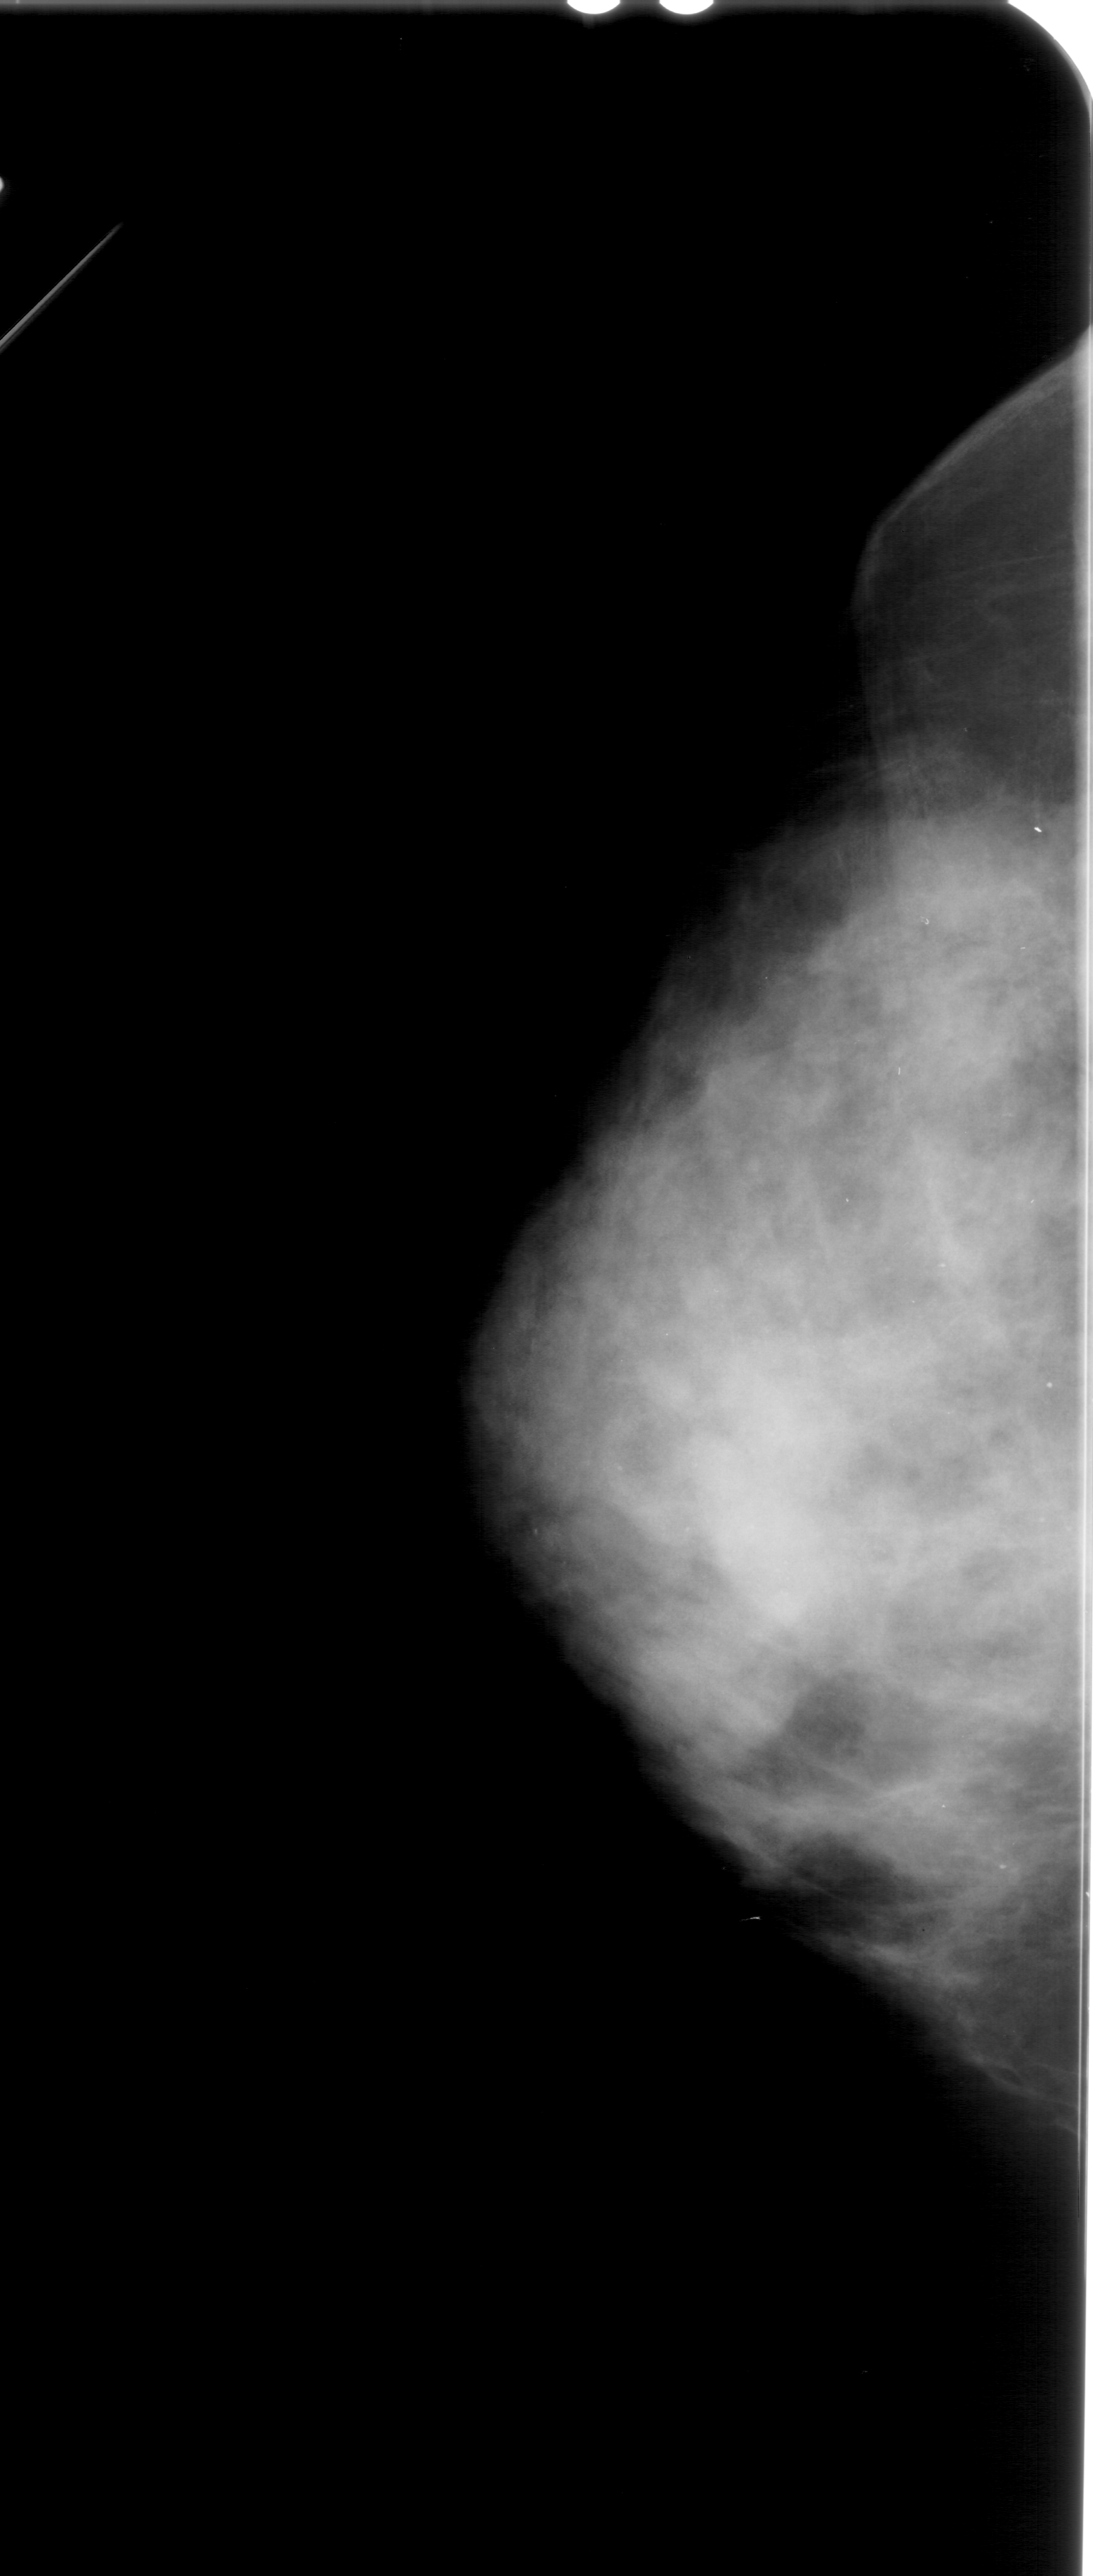
Scanned film-screen mammogram, left breast, craniocaudal (CC) view, breast composition: extremely dense (BI-RADS density category 4 of 4).
Marked abnormality: calcifications, morphology punctate, distribution segmental; BI-RADS assessment category 4; pathology (as recorded): malignant.